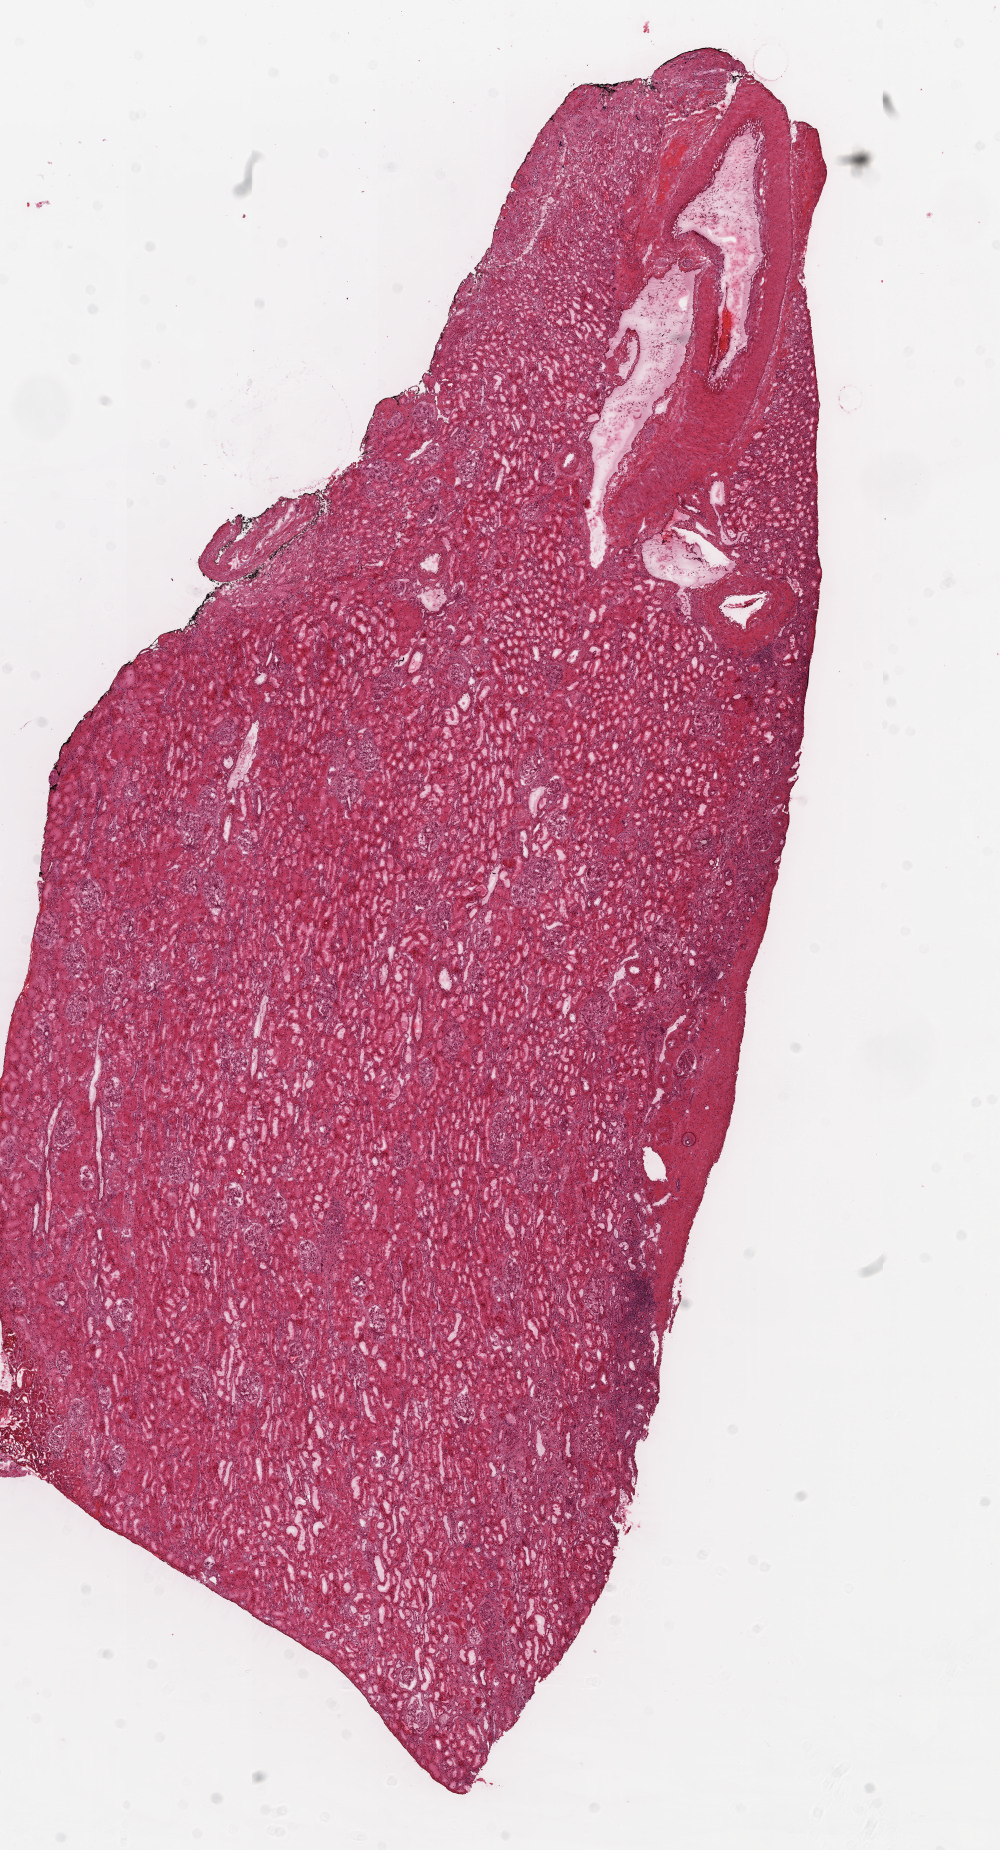
Whole-slide histology image, H&E-stained — low-resolution overview of the scanned area, about 8.0 x 14.8 mm. Frozen section from the top of the tissue portion. Kidney, solid tissue normal (non-tumour tissue) sample. Male, age 47 years at initial diagnosis.
This section: solid tissue normal (non-tumour) sample from the same patient. Patient diagnosis: Clear cell adenocarcinoma, NOS.